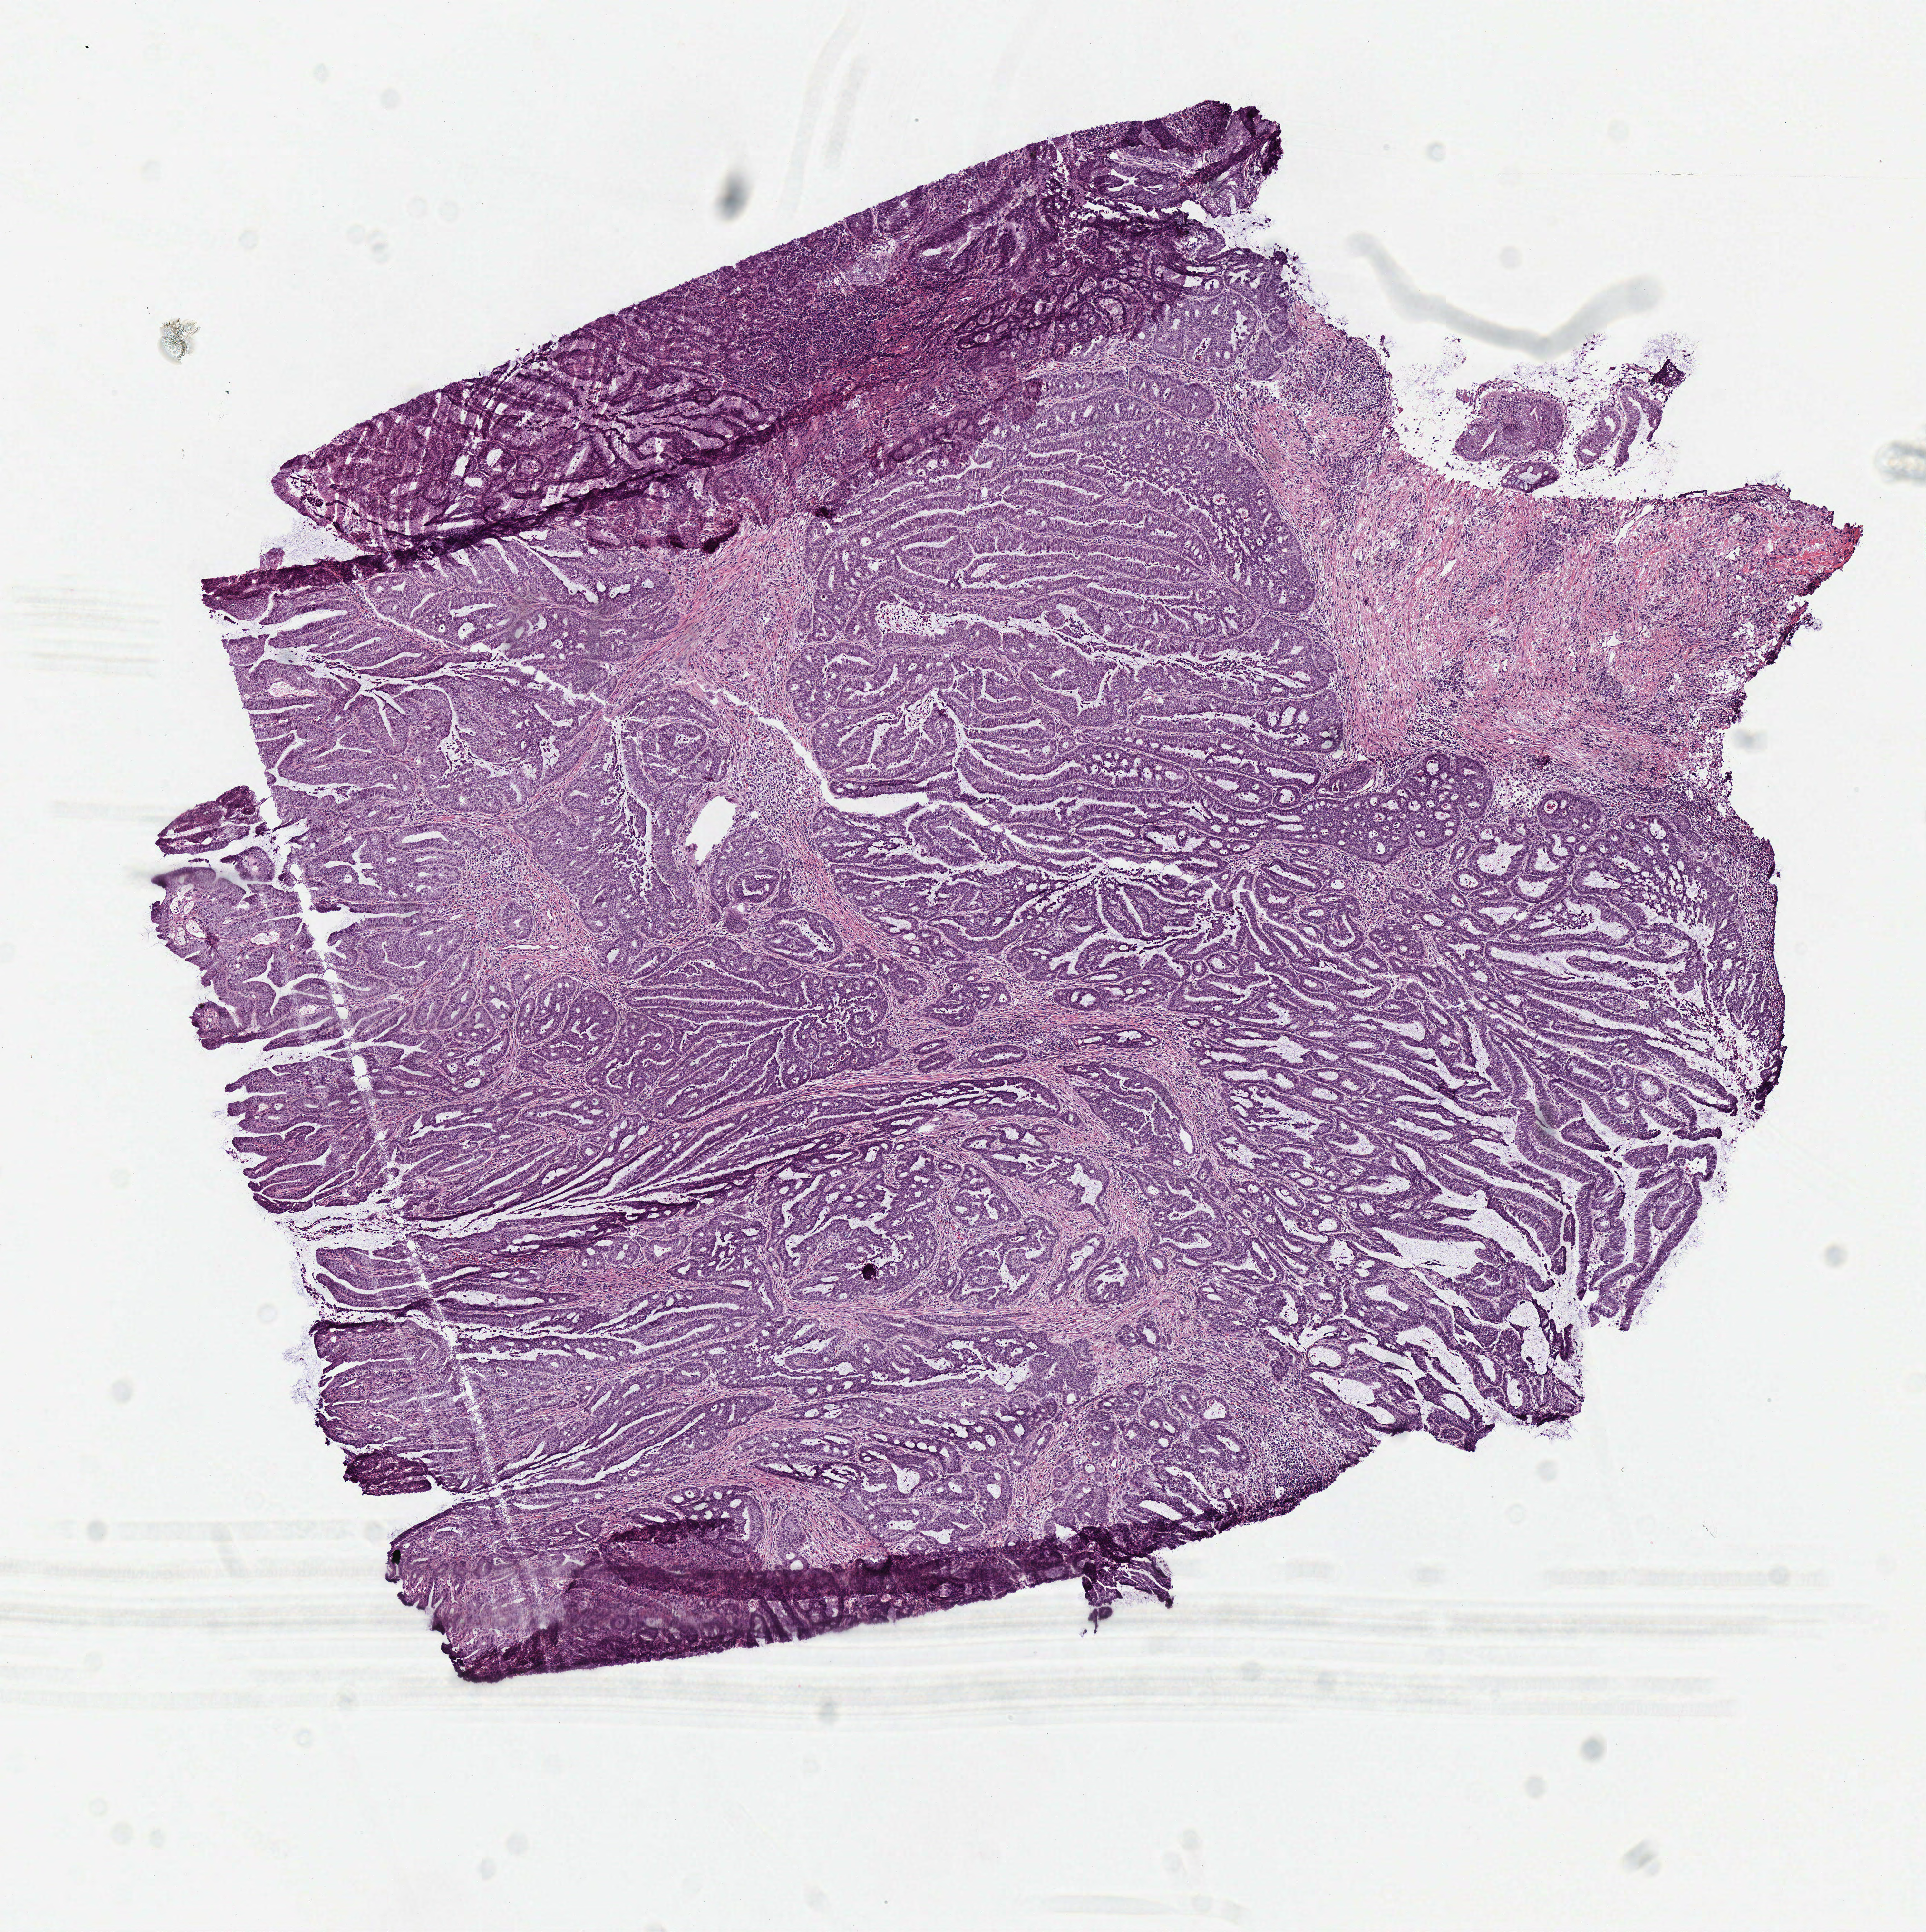
Hematoxylin and eosin (H&E) stained whole-slide image — shown as a low-resolution overview of the whole scanned area (about 5.9 x 5.9 mm, slide scanned at 40x); frozen section from the top of the tissue portion; colon, primary tumour sample. Female patient; age at initial diagnosis 60 years. Pathologist review of this section (percent, as recorded): tumour cells 80%, tumour nuclei 85%, normal cells 0%, stromal cells 15%, necrosis 5%.
Pathologic diagnosis: Adenocarcinoma, NOS (cecum). Lymph nodes positive (case pathology): 3 of 44 examined. AJCC pathologic stage: III (6th edition).